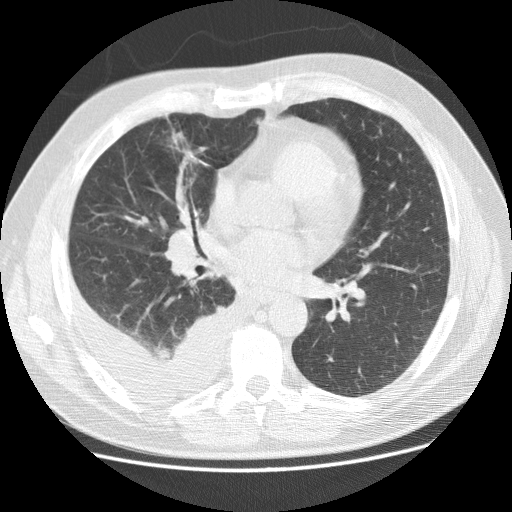
Low-dose screening chest CT, one axial slice; reconstruction kernel STANDARD; 120 kVp; lung window (W 1500 / L -600 HU); 2.5 mm slice thickness; 512 × 512 image matrix, field of view 380 × 380 mm.
Outlined on this slice (outlined manually by an expert reader):
- lesion 1 (tumor, middle lobe of right lung): bounding box <171,131,193,152> (left, top, right, bottom; pixels)